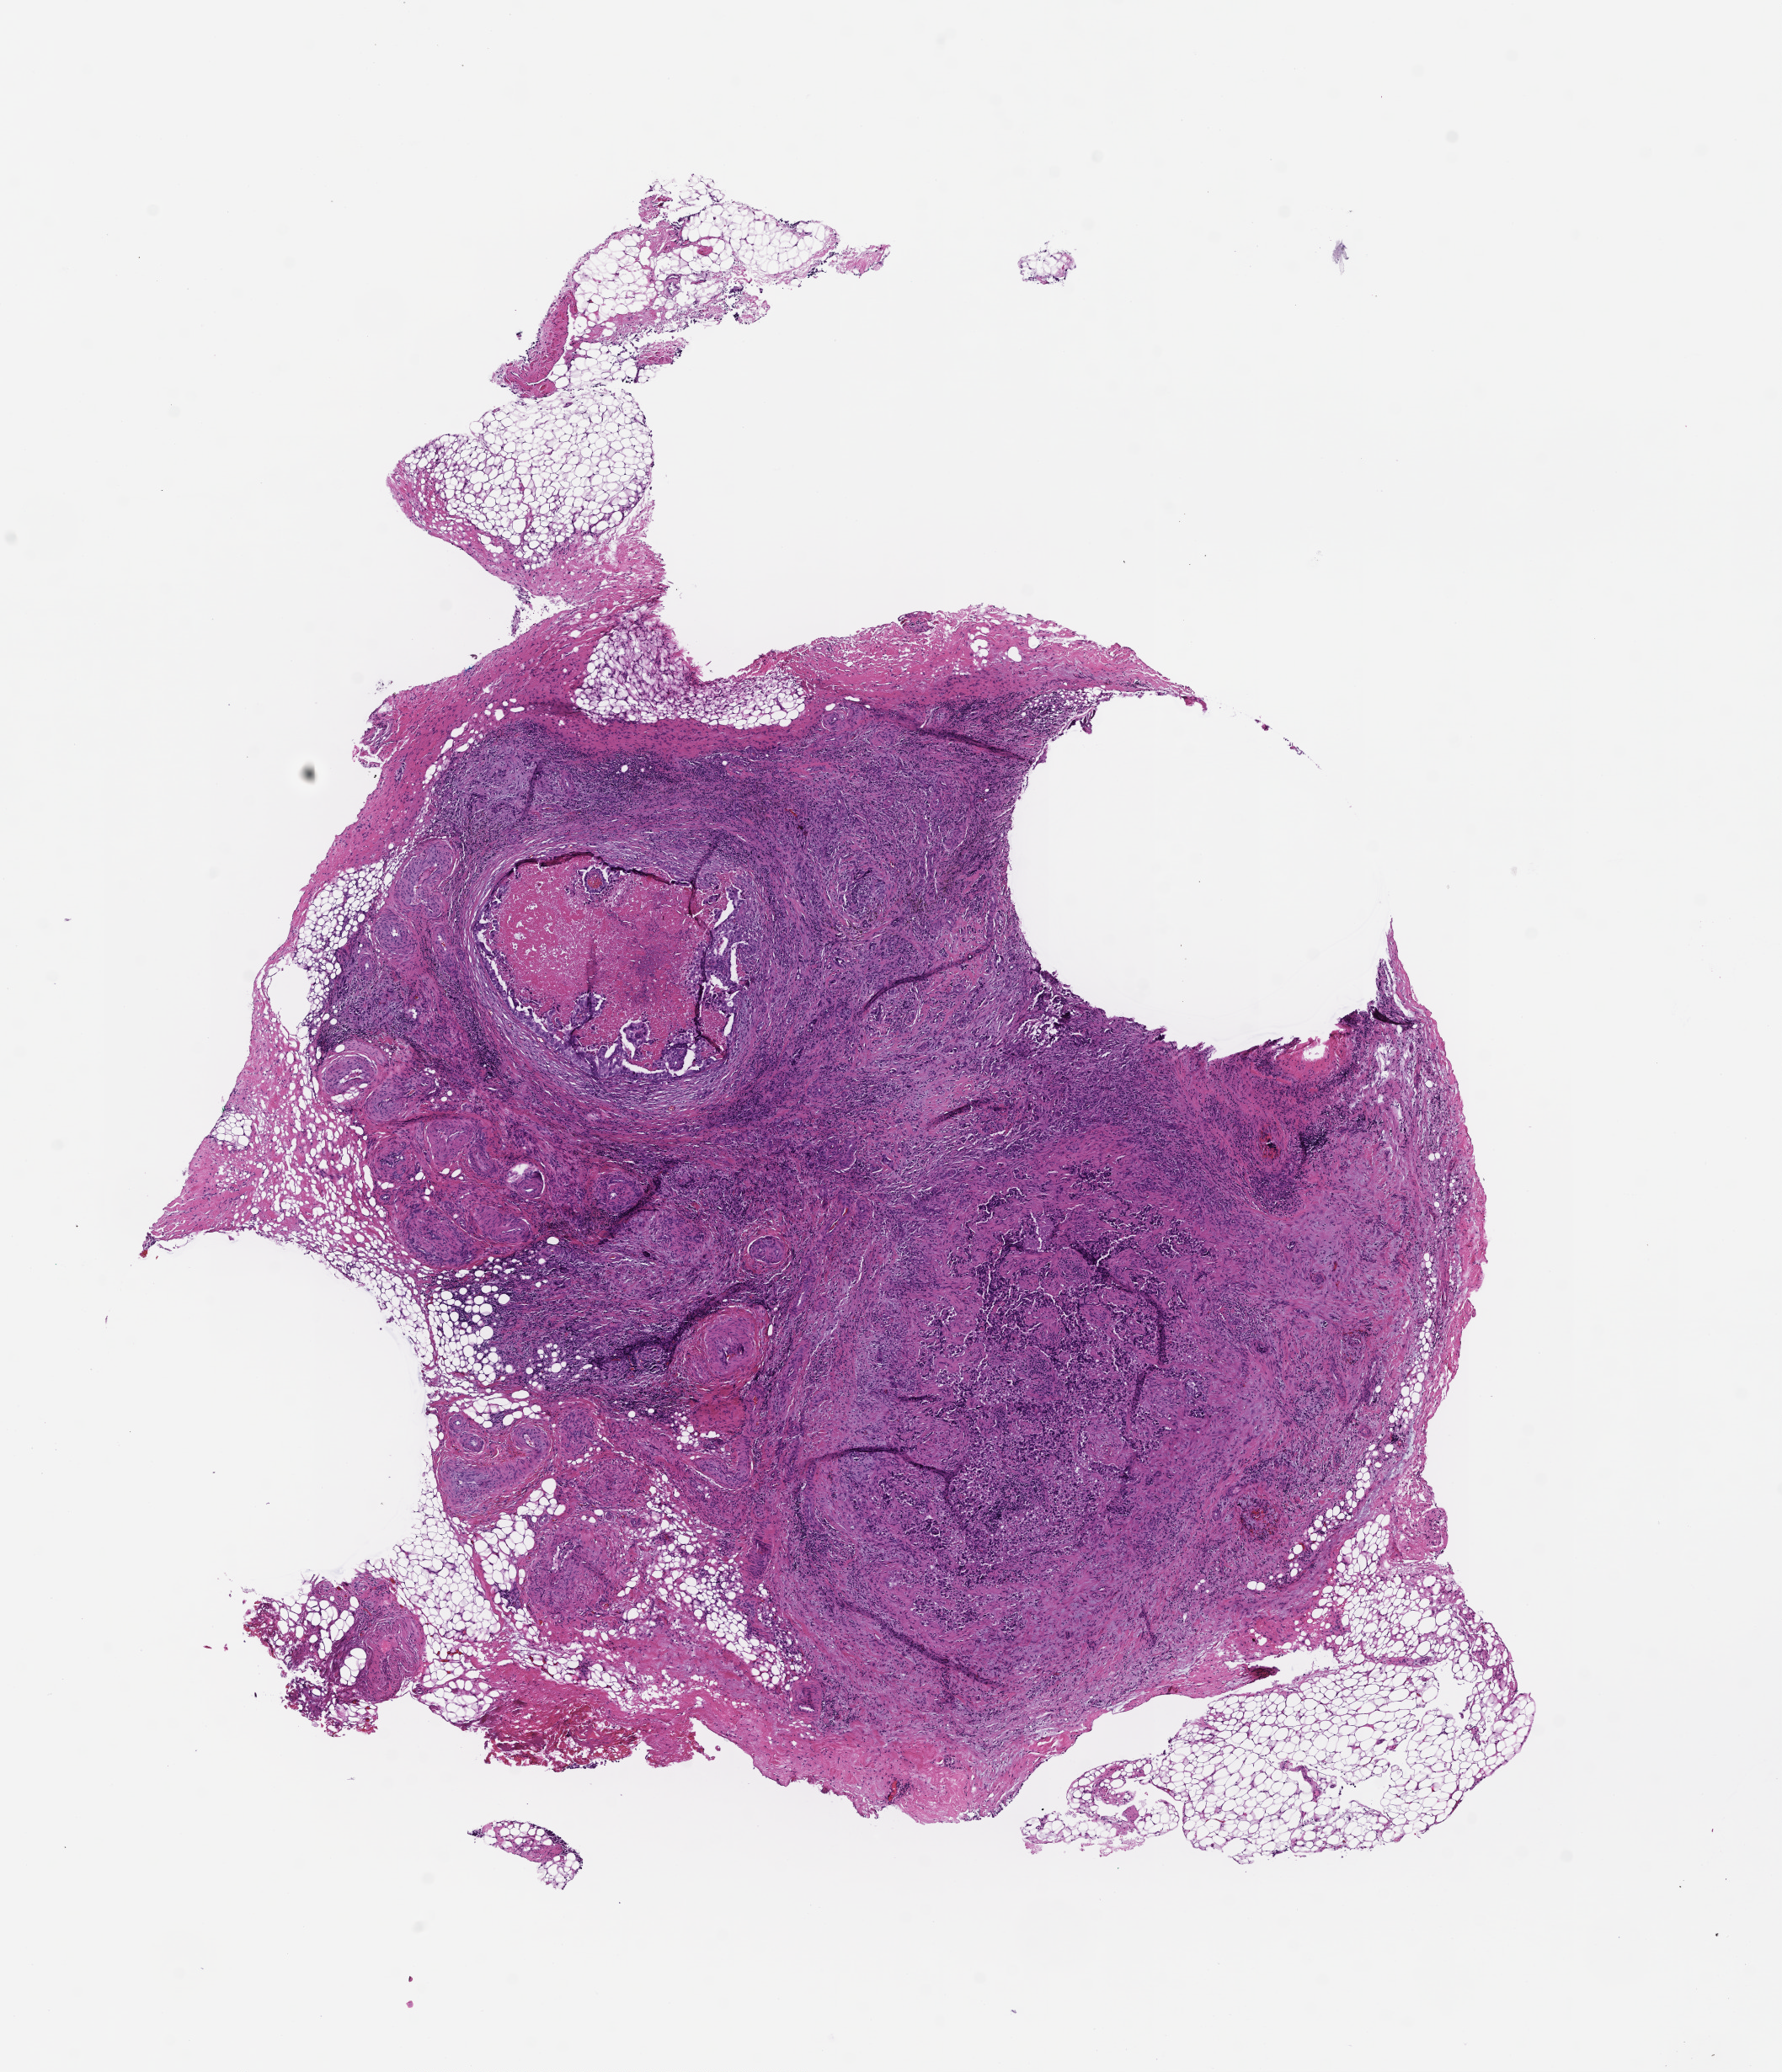
H&E whole-slide image — whole scanned area (about 8.5 x 9.9 mm) shown as a low-resolution overview; formalin-fixed, paraffin-embedded (FFPE) tissue. Patient: female.
This section: metastatic tumor tissue. Primary diagnosis of the patient: Non-Small Cell Lung Carcinoma.